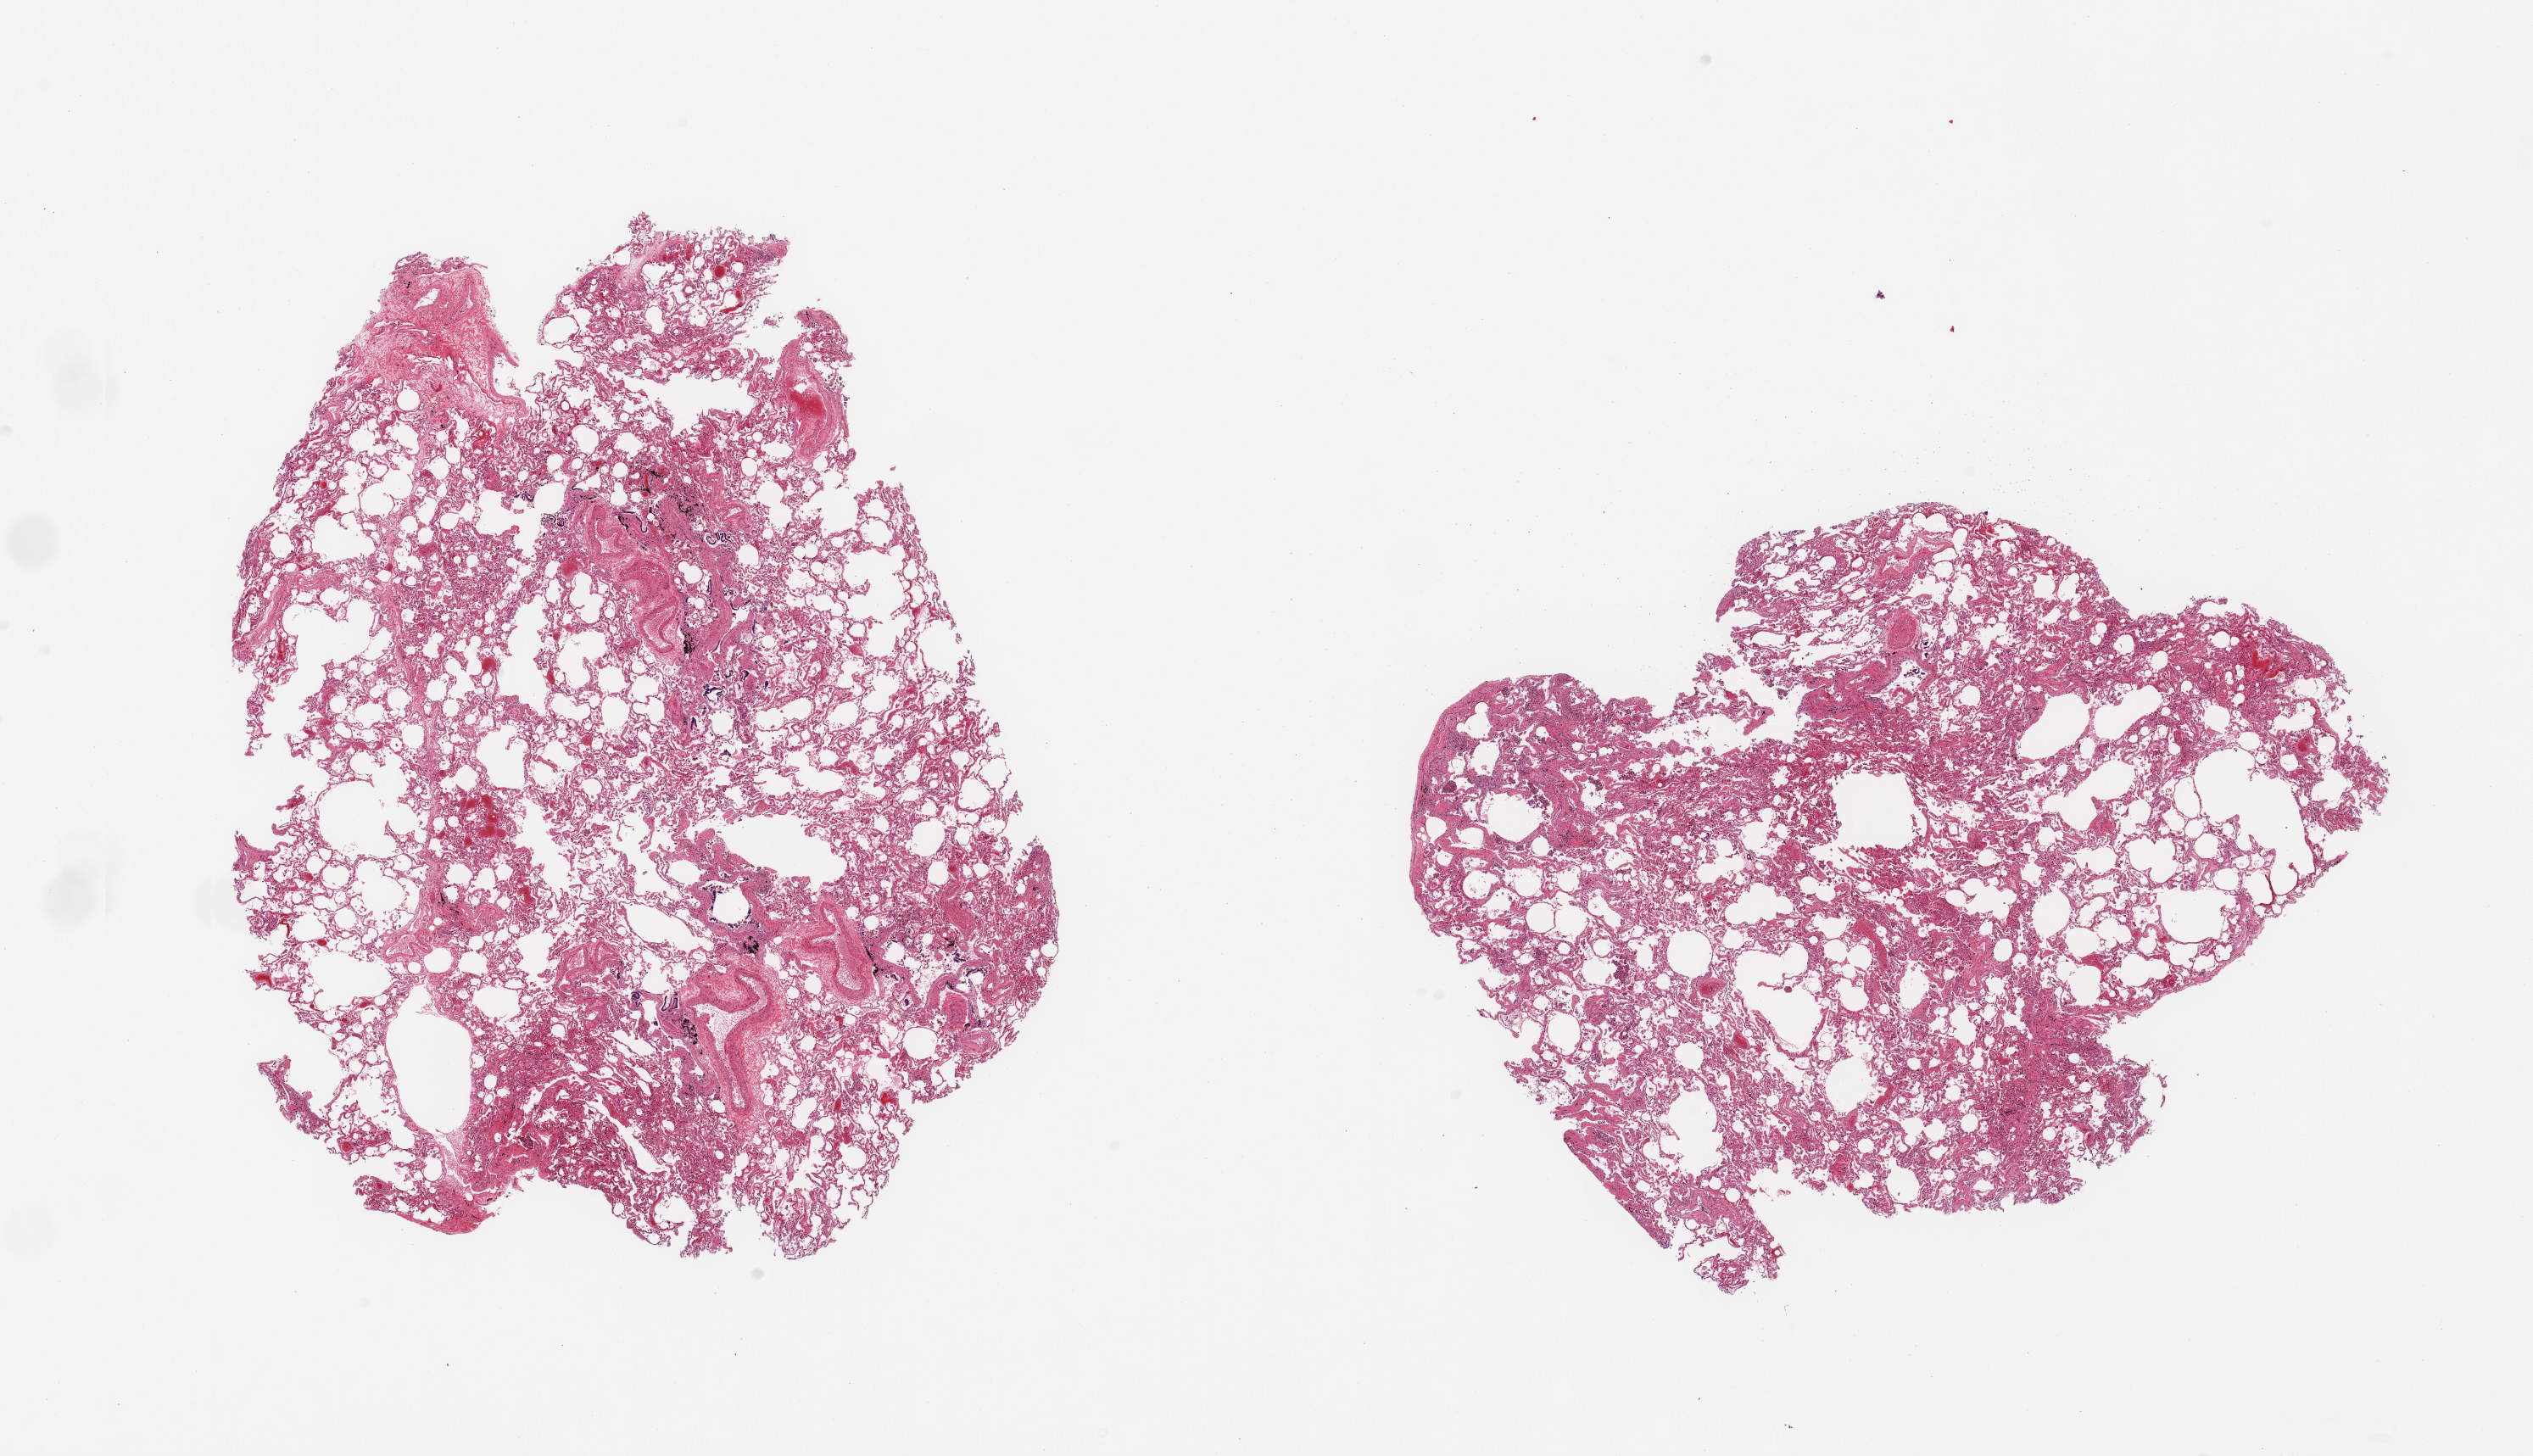
Haematoxylin and eosin whole-slide image — shown as a low-resolution overview of the whole scanned area (about 23.6 x 13.6 mm, from a 20x scan), PAXgene-fixed paraffin-embedded (PFPE) section, section of lung (target tissue), donor tissue sample. Donor: male.
• review note (as recorded): 2 pieces, emphysematous changes